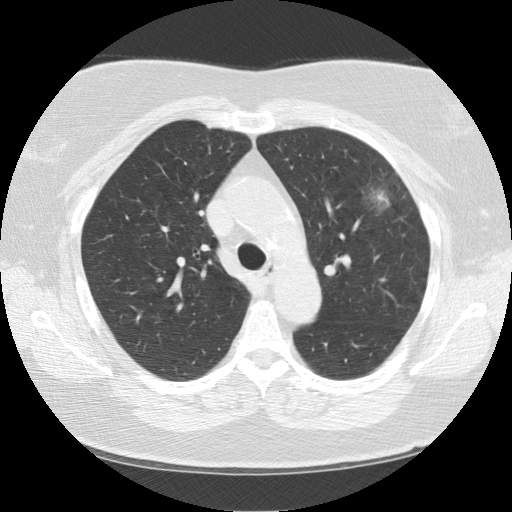
Chest CT (low-dose screening protocol), one axial image; baseline annual screen; lung window (W 1500 / L -600 HU); 512 × 512 image matrix. Female participant, aged 67 years at enrolment. Former smoker at enrolment.
- Expert reader's lesion annotation, bounding box (x1, y1, x2, y2) in pixels: (344, 153, 423, 231).
- Reader record for this screening exam (exam-level; its link to the box is not recorded): non-calcified nodule or mass ≥4 mm, left upper lobe, 28 × 19 mm, soft tissue attenuation.
- Official screen result: positive, change unspecified: nodule(s) >= 4 mm or enlarging nodule(s), mass(es), or other non-specific abnormalities suspicious for lung cancer.
- Lung cancer was diagnosed 33 days after this screen: squamous cell carcinoma, NOS, left upper lobe, poorly differentiated (G3), stage IA (AJCC 6th edition), 25 mm at pathology.